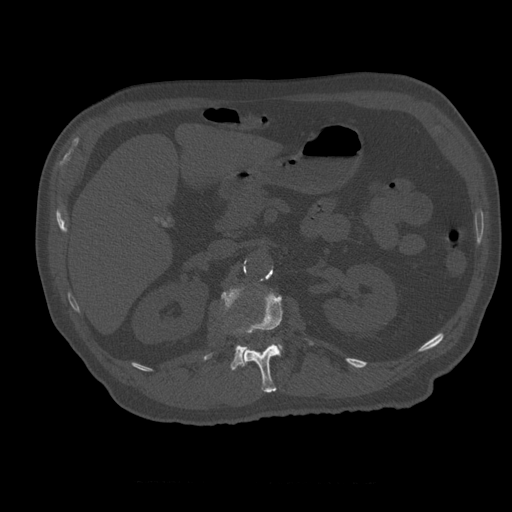
CT including the spine, one axial slice. Slice 230 of 399 in the series (ordered by position). Reconstruction kernel STANDARD. 120 kVp. Bone window (W 1800 / L 400 HU). 1.25 mm slice thickness. 512 × 512 image matrix, field of view 407 × 407 mm. Patient age 73 years. From the clinical record (not read from this slice): primary cancer: prostate; vertebrae with lytic lesions (as recorded): L2.
Structures marked on this image (semi-automatic segmentation, software-assisted and operator-edited):
- L1 vertebra: bounding box (x1, y1, x2, y2) in pixels: (243, 291, 314, 393)
- L2 vertebra: (204, 289, 247, 370)